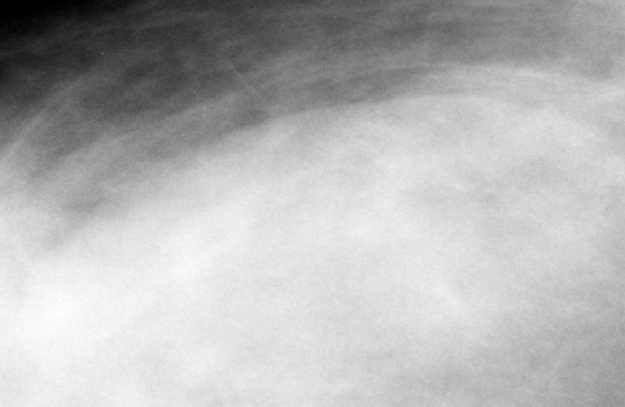
Region of interest cut from a scanned film mammogram (one marked finding); right breast; CC view; BI-RADS breast density category 3 (scale 1–4).
Mass, shape oval, margins circumscribed / obscured; BI-RADS assessment category 3; subtlety rating 3 on a 1 (subtle) to 5 (obvious) scale; pathology result (as recorded, not read from the image): benign.